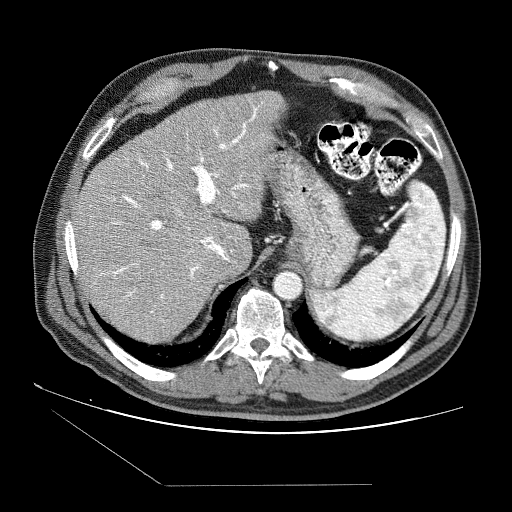
Contrast-enhanced abdominal CT (liver protocol), one axial slice; position 59 of 87 along the scan axis; soft-tissue window (W 400 / L 40 HU); 2.5 mm slice thickness; 512 × 512 image matrix, field of view 400 × 400 mm. Case-level facts recorded for this patient, not image findings: diagnosis: hepatocellular carcinoma (patient treated with transarterial chemoembolisation; whether this scan precedes or follows treatment is not stated here); TNM stage (as recorded): Stage-II; Child-Pugh class: B; tumour differentiation: no biopsy.
Annotated regions visible in this slice (semi-automatic segmentation, software-assisted and operator-edited):
- liver parenchyma outside the tumour (the mass and vessels are separate outlines, so this box may not span the whole liver): bounding box (x1, y1, x2, y2) in pixels: (74, 90, 286, 342)
- liver vessels: (94, 107, 259, 313)